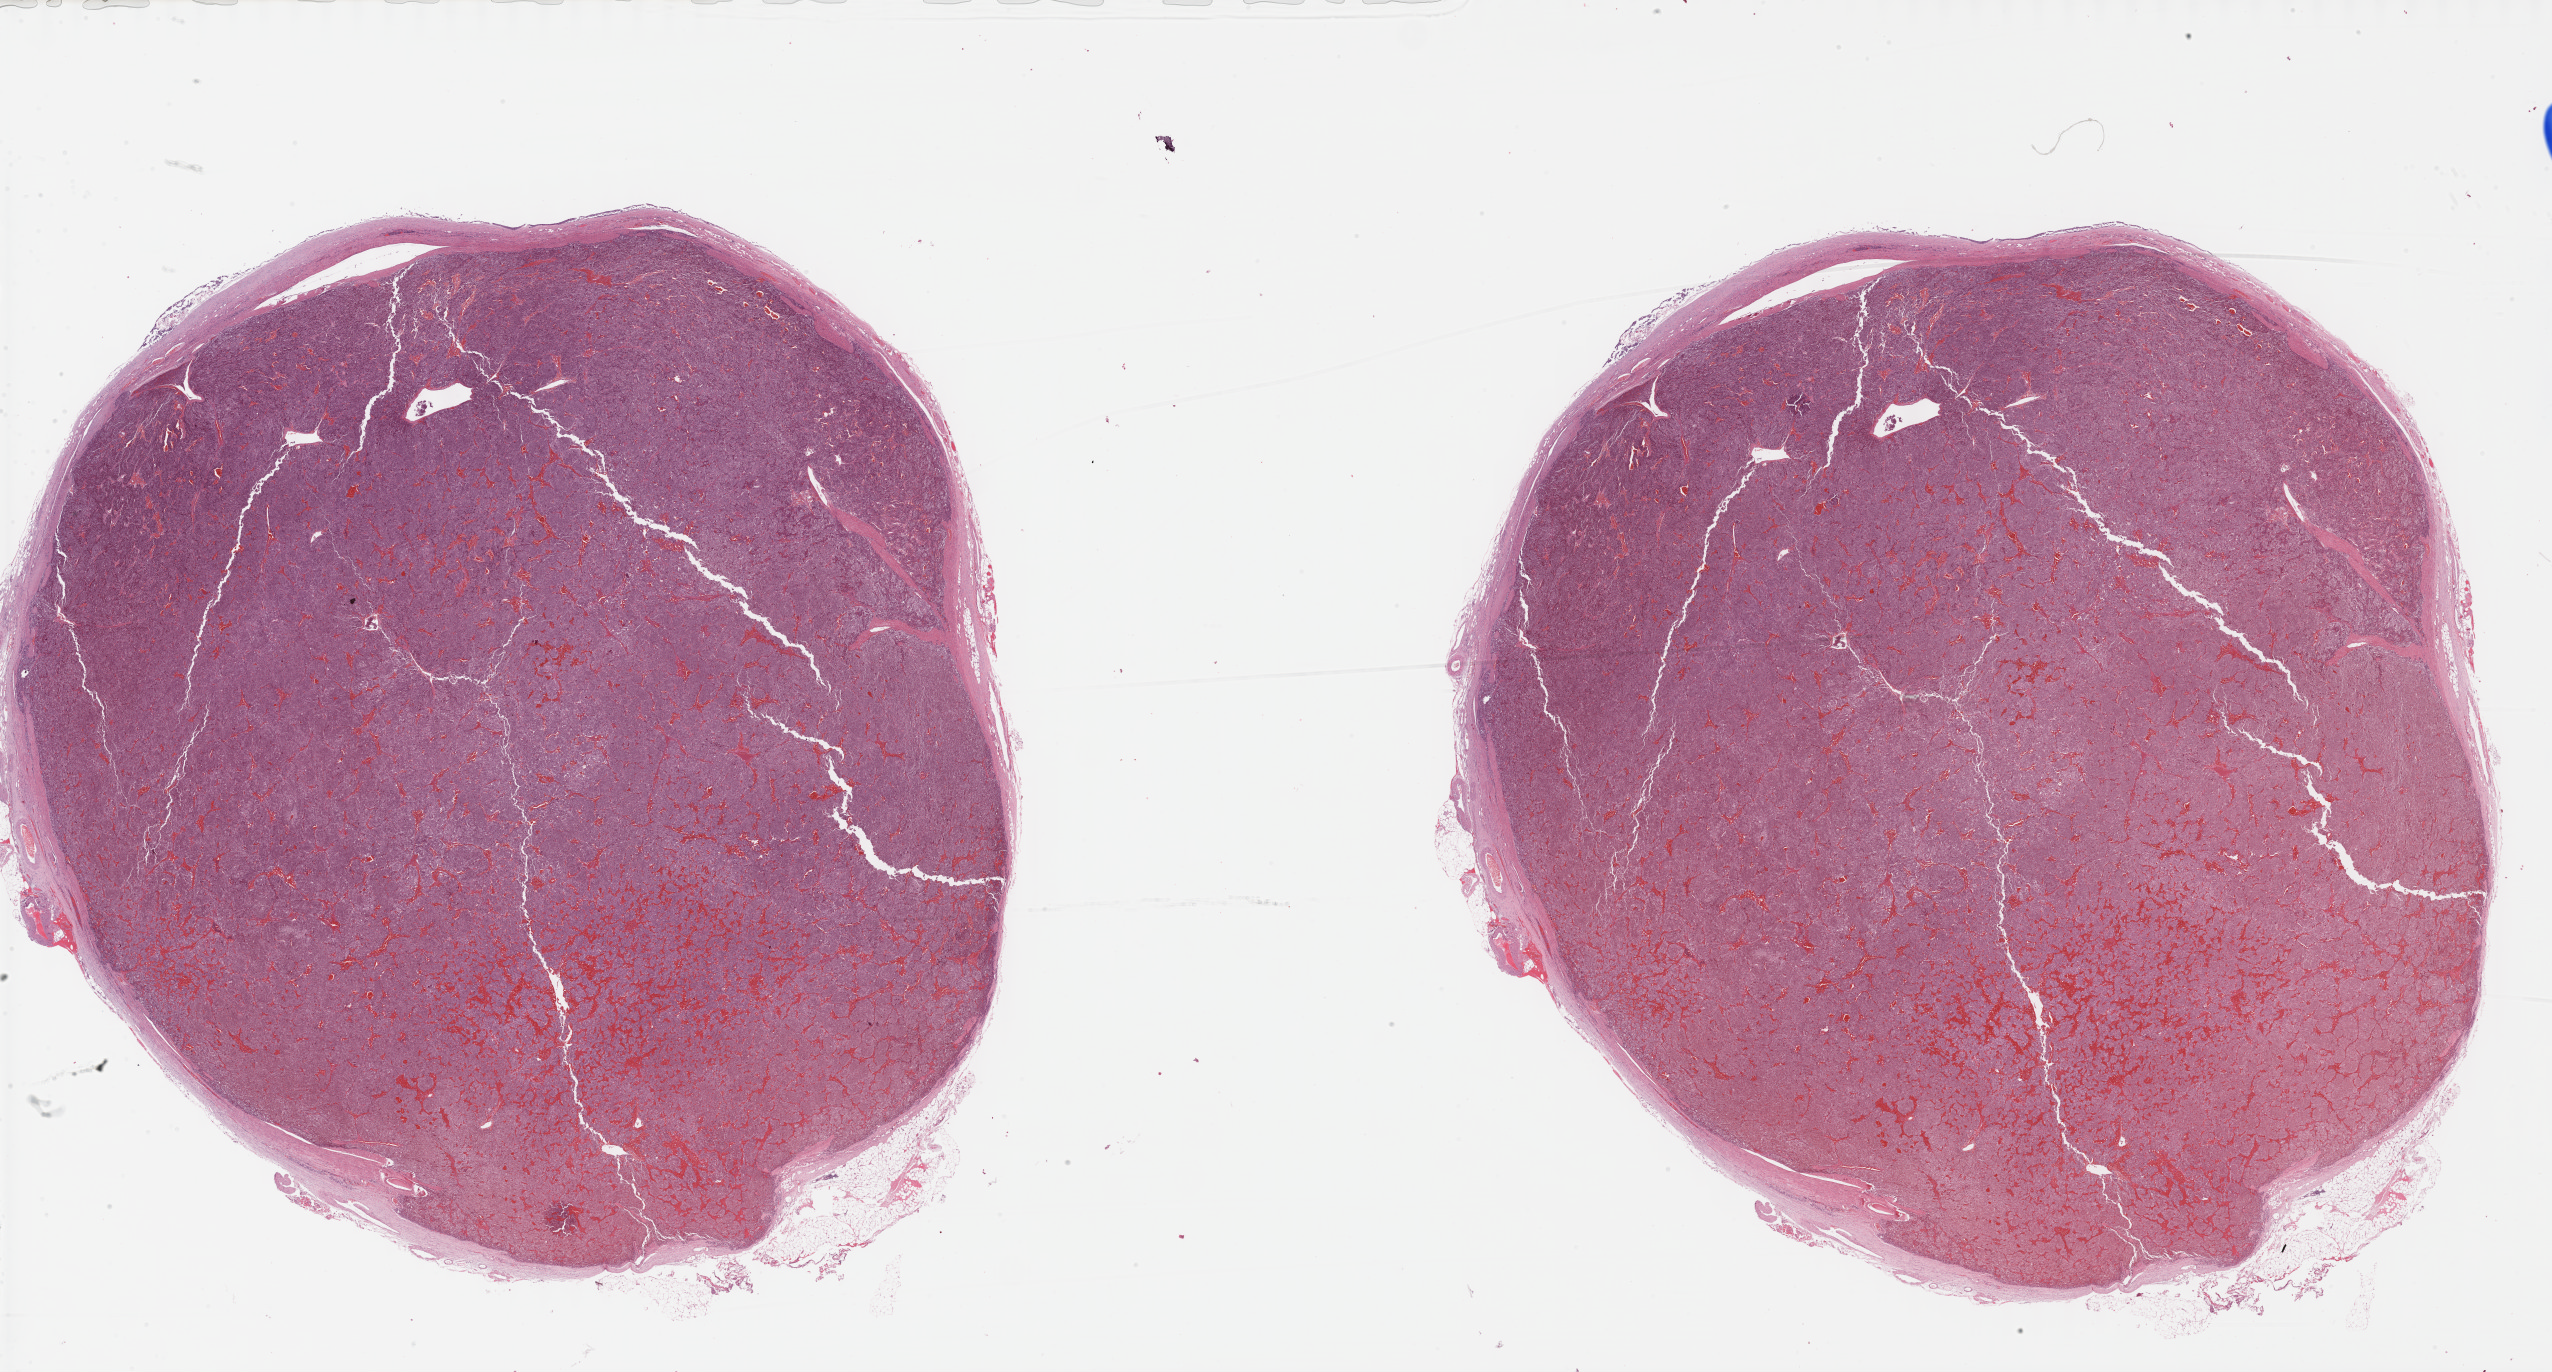
Hematoxylin and eosin (H&E) stained whole-slide image — whole scanned area (about 41.2 x 22.2 mm, slide scanned at 40x) shown as a low-resolution overview, FFPE section, adrenal gland, primary tumour sample. Patient: male, age at initial diagnosis 62 years.
- lymph nodes positive (case pathology): 2 of 2 examined
- histologic diagnosis: Pheochromocytoma, malignant